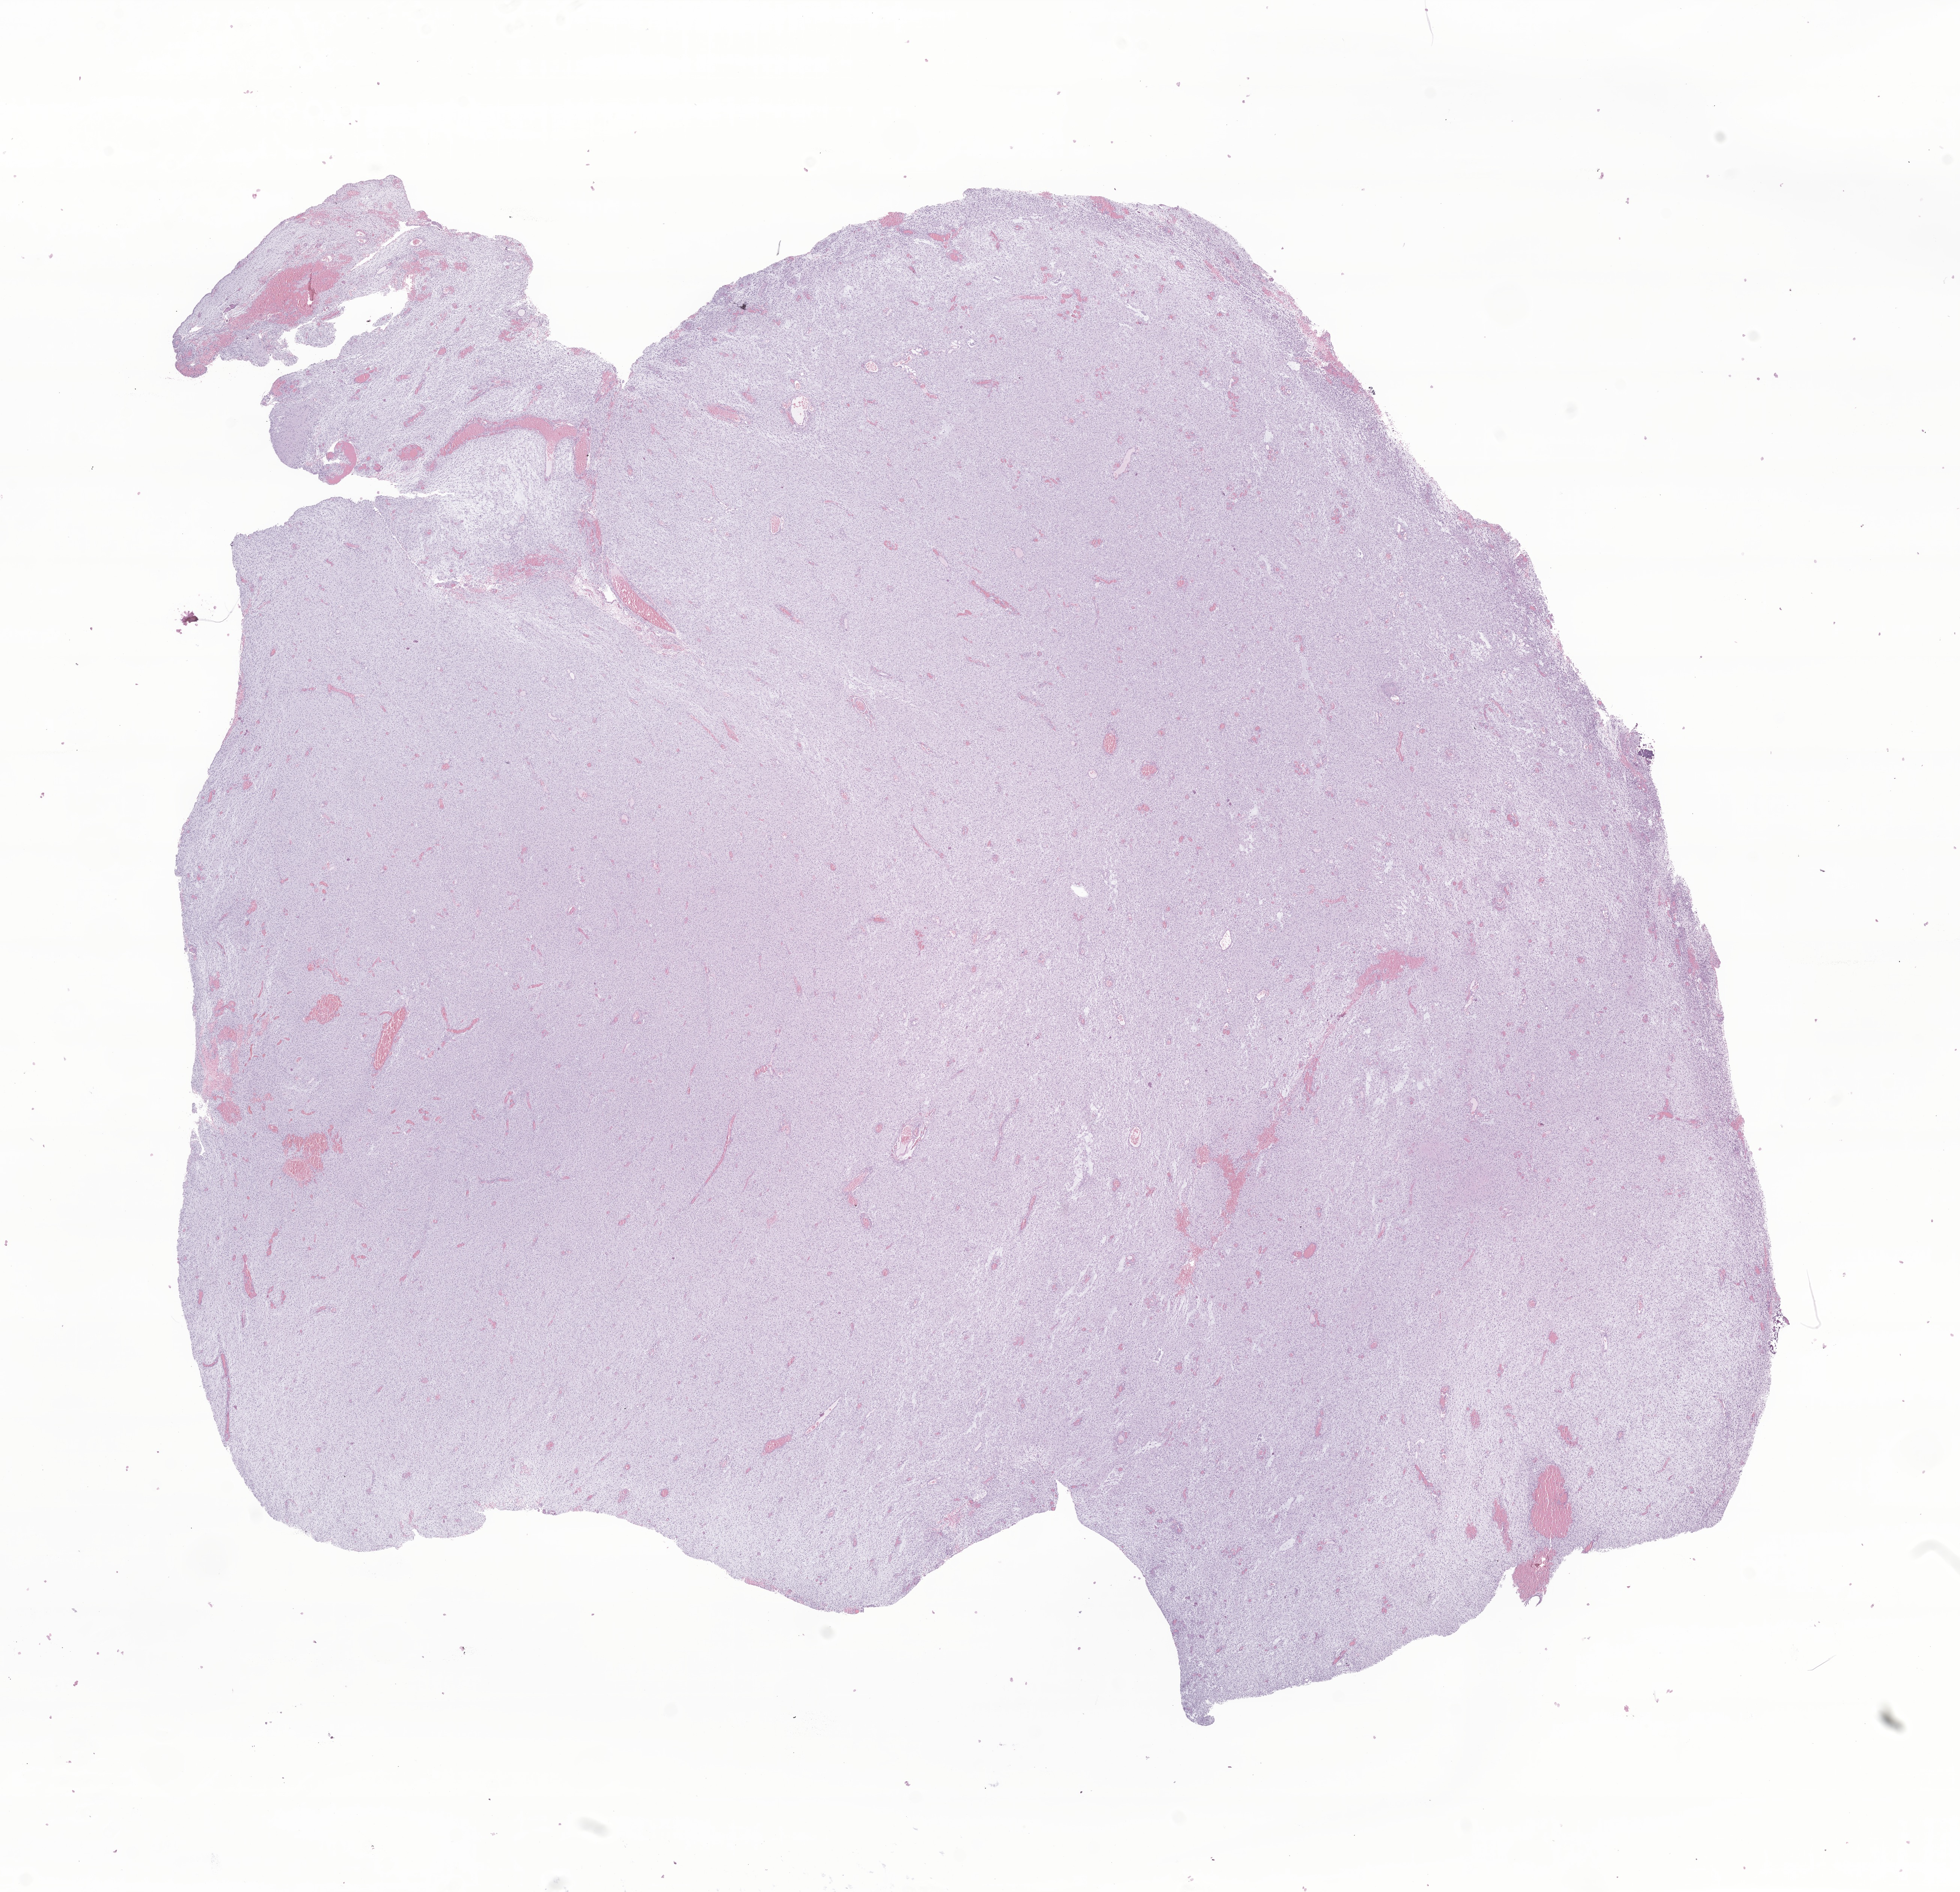
Whole-slide image, haematoxylin and eosin stain of tumor tissue from the cerebral ventricle, whole scanned area (about 22.0 x 21.2 mm) shown as a low-resolution overview, formalin-fixed, paraffin-embedded (FFPE) tissue. Female patient, age 63 months (5 years 3 months).
Recorded diagnosis: Pilocytic astrocytoma.